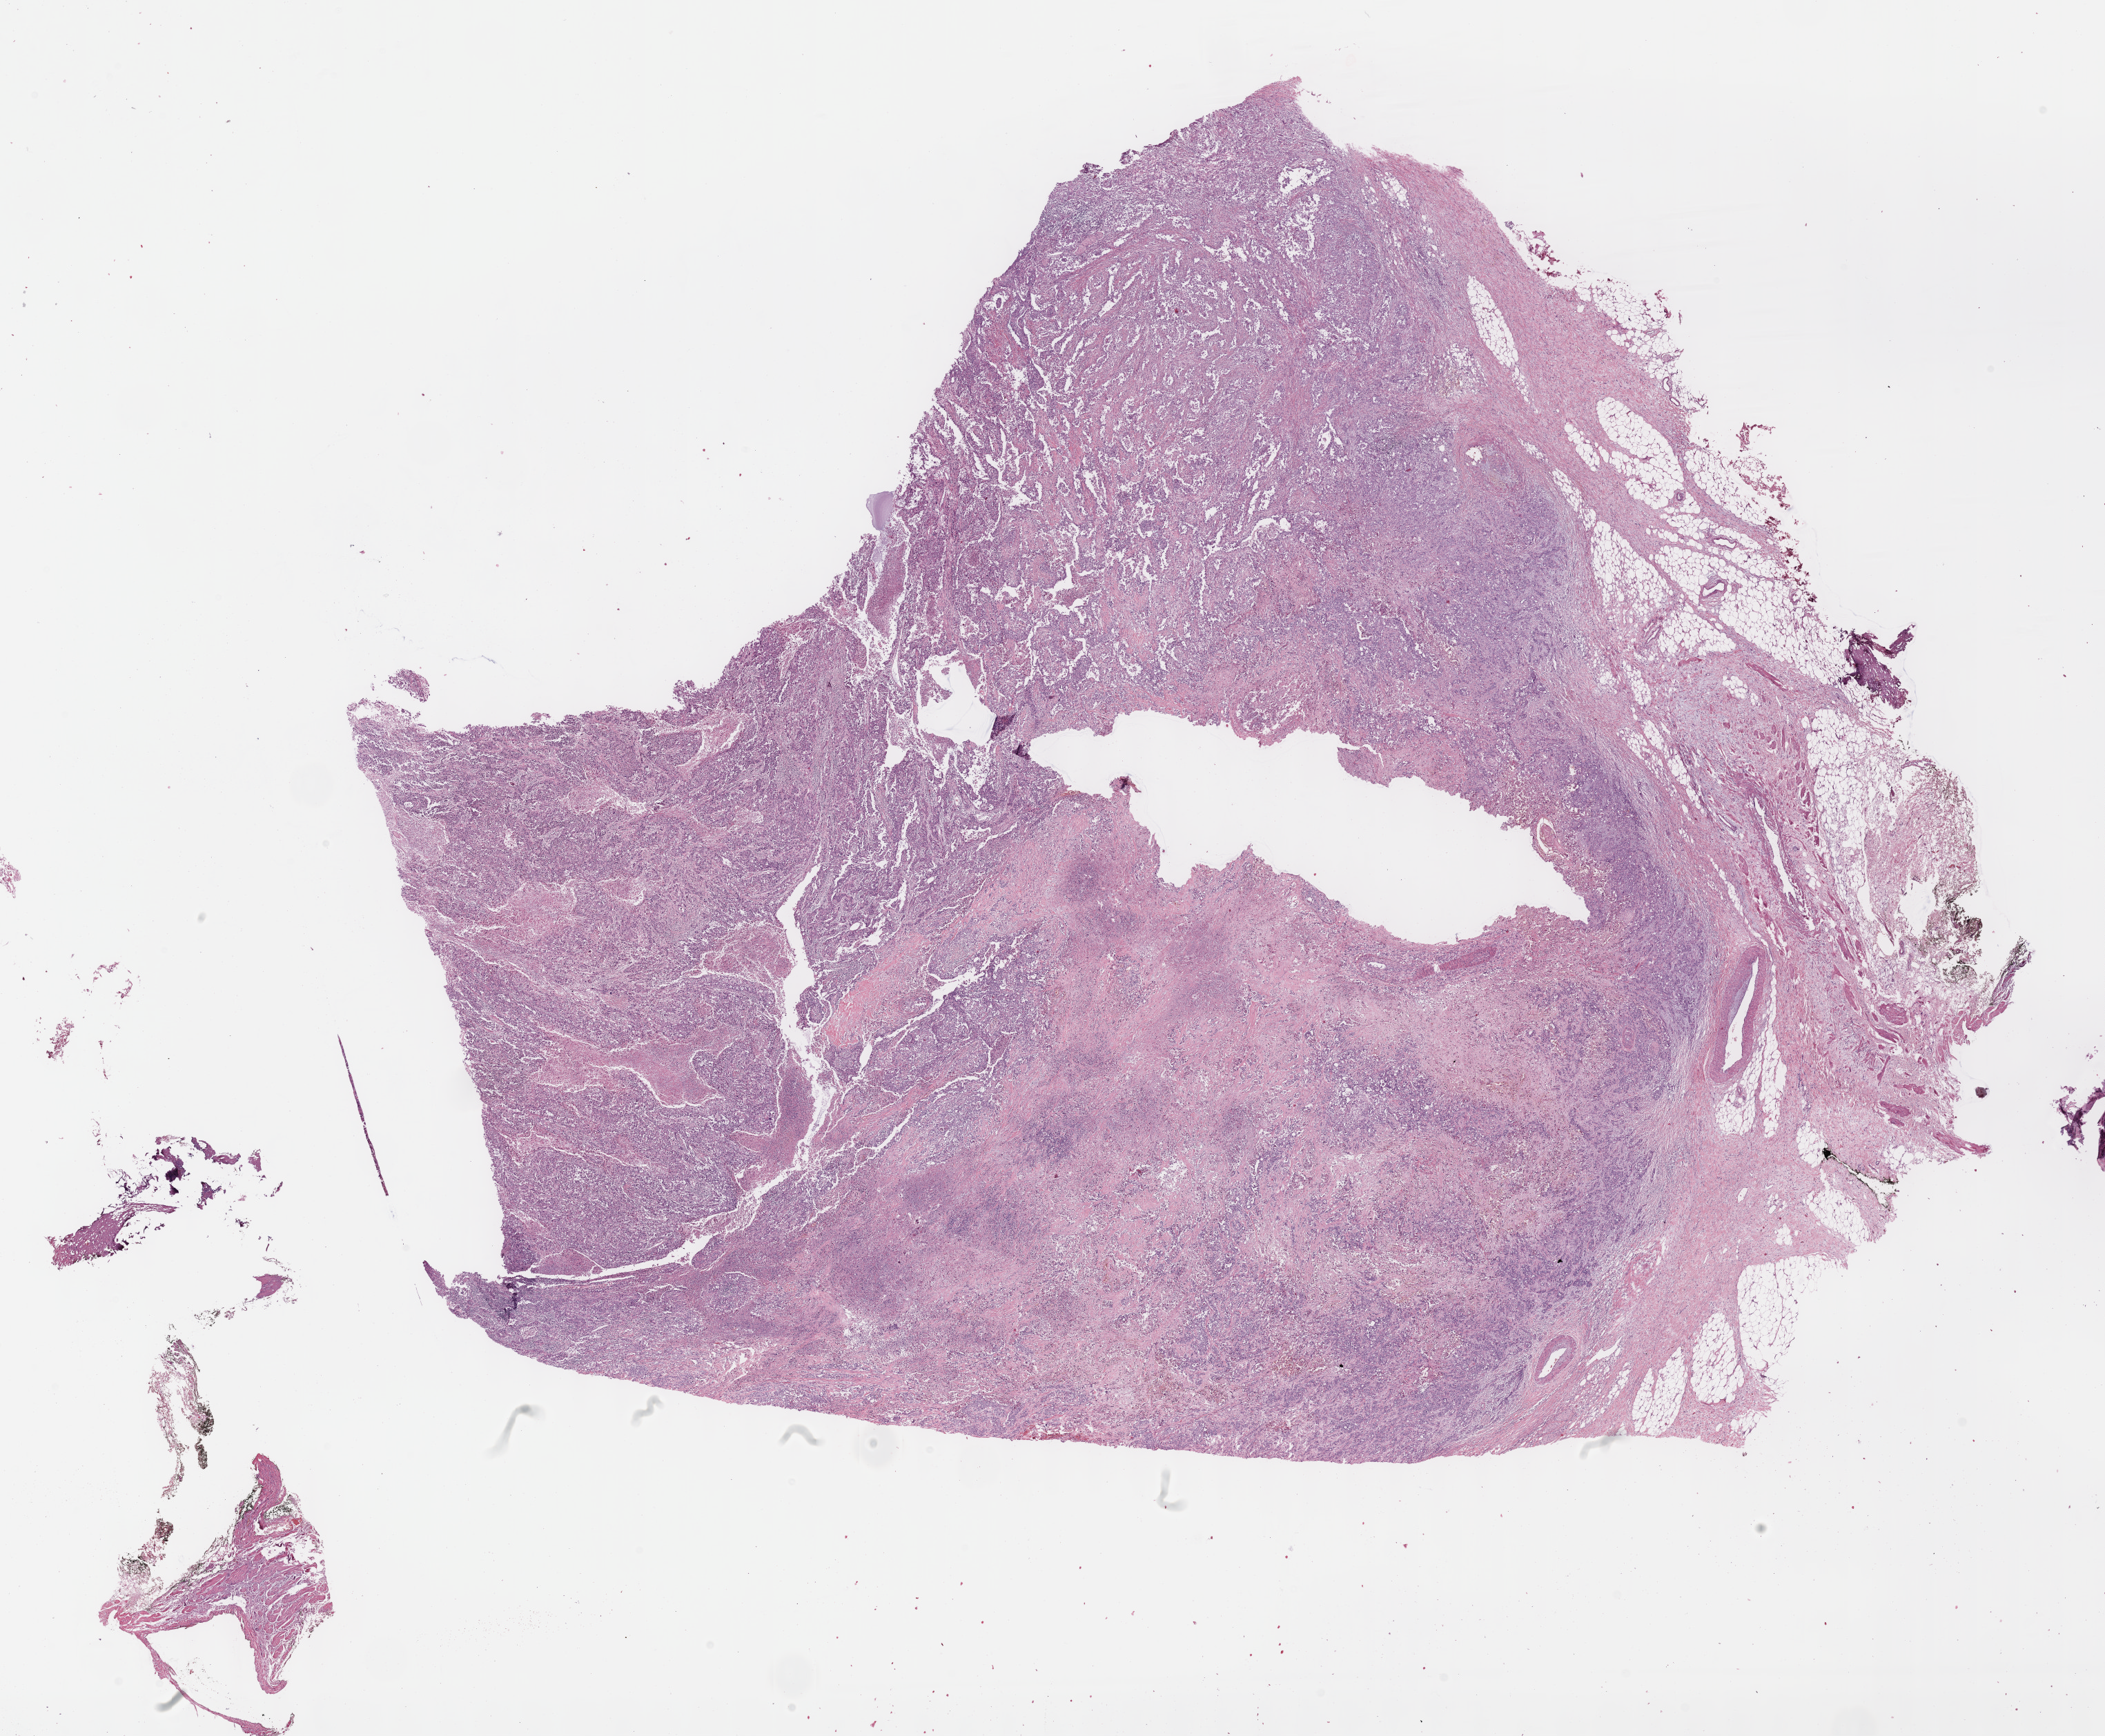
H&E-stained whole-slide image, a low-resolution overview of the entire scanned area, about 24.6 x 20.3 mm (acquisition: 40x scan). FFPE section. Sample: primary tumour, bladder. Male patient; age at initial diagnosis 80 years. Histologic grade: high grade.
Lymph nodes positive (case pathology): 0 of 6 examined. Diagnosis: Papillary transitional cell carcinoma (posterior wall of bladder). AJCC pathologic stage: II (7th edition). TNM: T2b N0 M0.